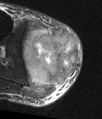
MRI of an extremity soft-tissue mass, one axial slice. Position 29 of 48 along the scan axis. T2-weighted fat-saturated. MR volume resampled by the dataset authors to the PET/CT grid (not the native acquisition matrix). 3.27 mm slice thickness. 102 × 119 image matrix, field of view 100 × 116 mm. Male patient. From the clinical record (not read from this slice): histological type: pleiomorphic liposarcoma; grade: high; site of the primary tumour: right calf.
Annotated regions visible in this slice (expert contour drawn on MRI and transferred to this co-registered scan by the dataset authors):
- gross tumour volume including surrounding oedema: bounding box <23,28,77,90> (left, top, right, bottom; pixels)
- gross tumour volume (mass): <23,30,77,86>